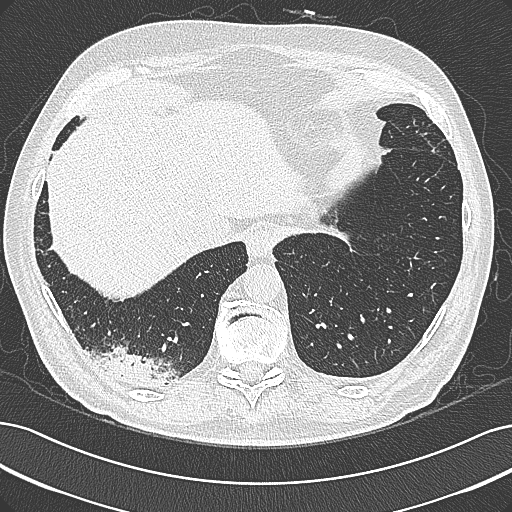
Axial slice from a low-dose chest CT screening exam; baseline annual screen; lung window (W 1500 / L -600 HU); 1 mm slice thickness. Male participant, aged 68 years at enrolment. Former smoker at enrolment.
Expert-annotated lung lesion, bounding box [x1, y1, x2, y2] px = [96, 339, 187, 400]. No non-calcified nodule or mass ≥4 mm was recorded by the screening reader at this exam. Official screen result: negative screen, significant abnormalities not suspicious for lung cancer. Lung cancer was diagnosed 154 days after this screen: mucinous adenocarcinoma, right lower lobe, well differentiated (G1), stage IB (AJCC 6th edition), 50 mm at pathology.